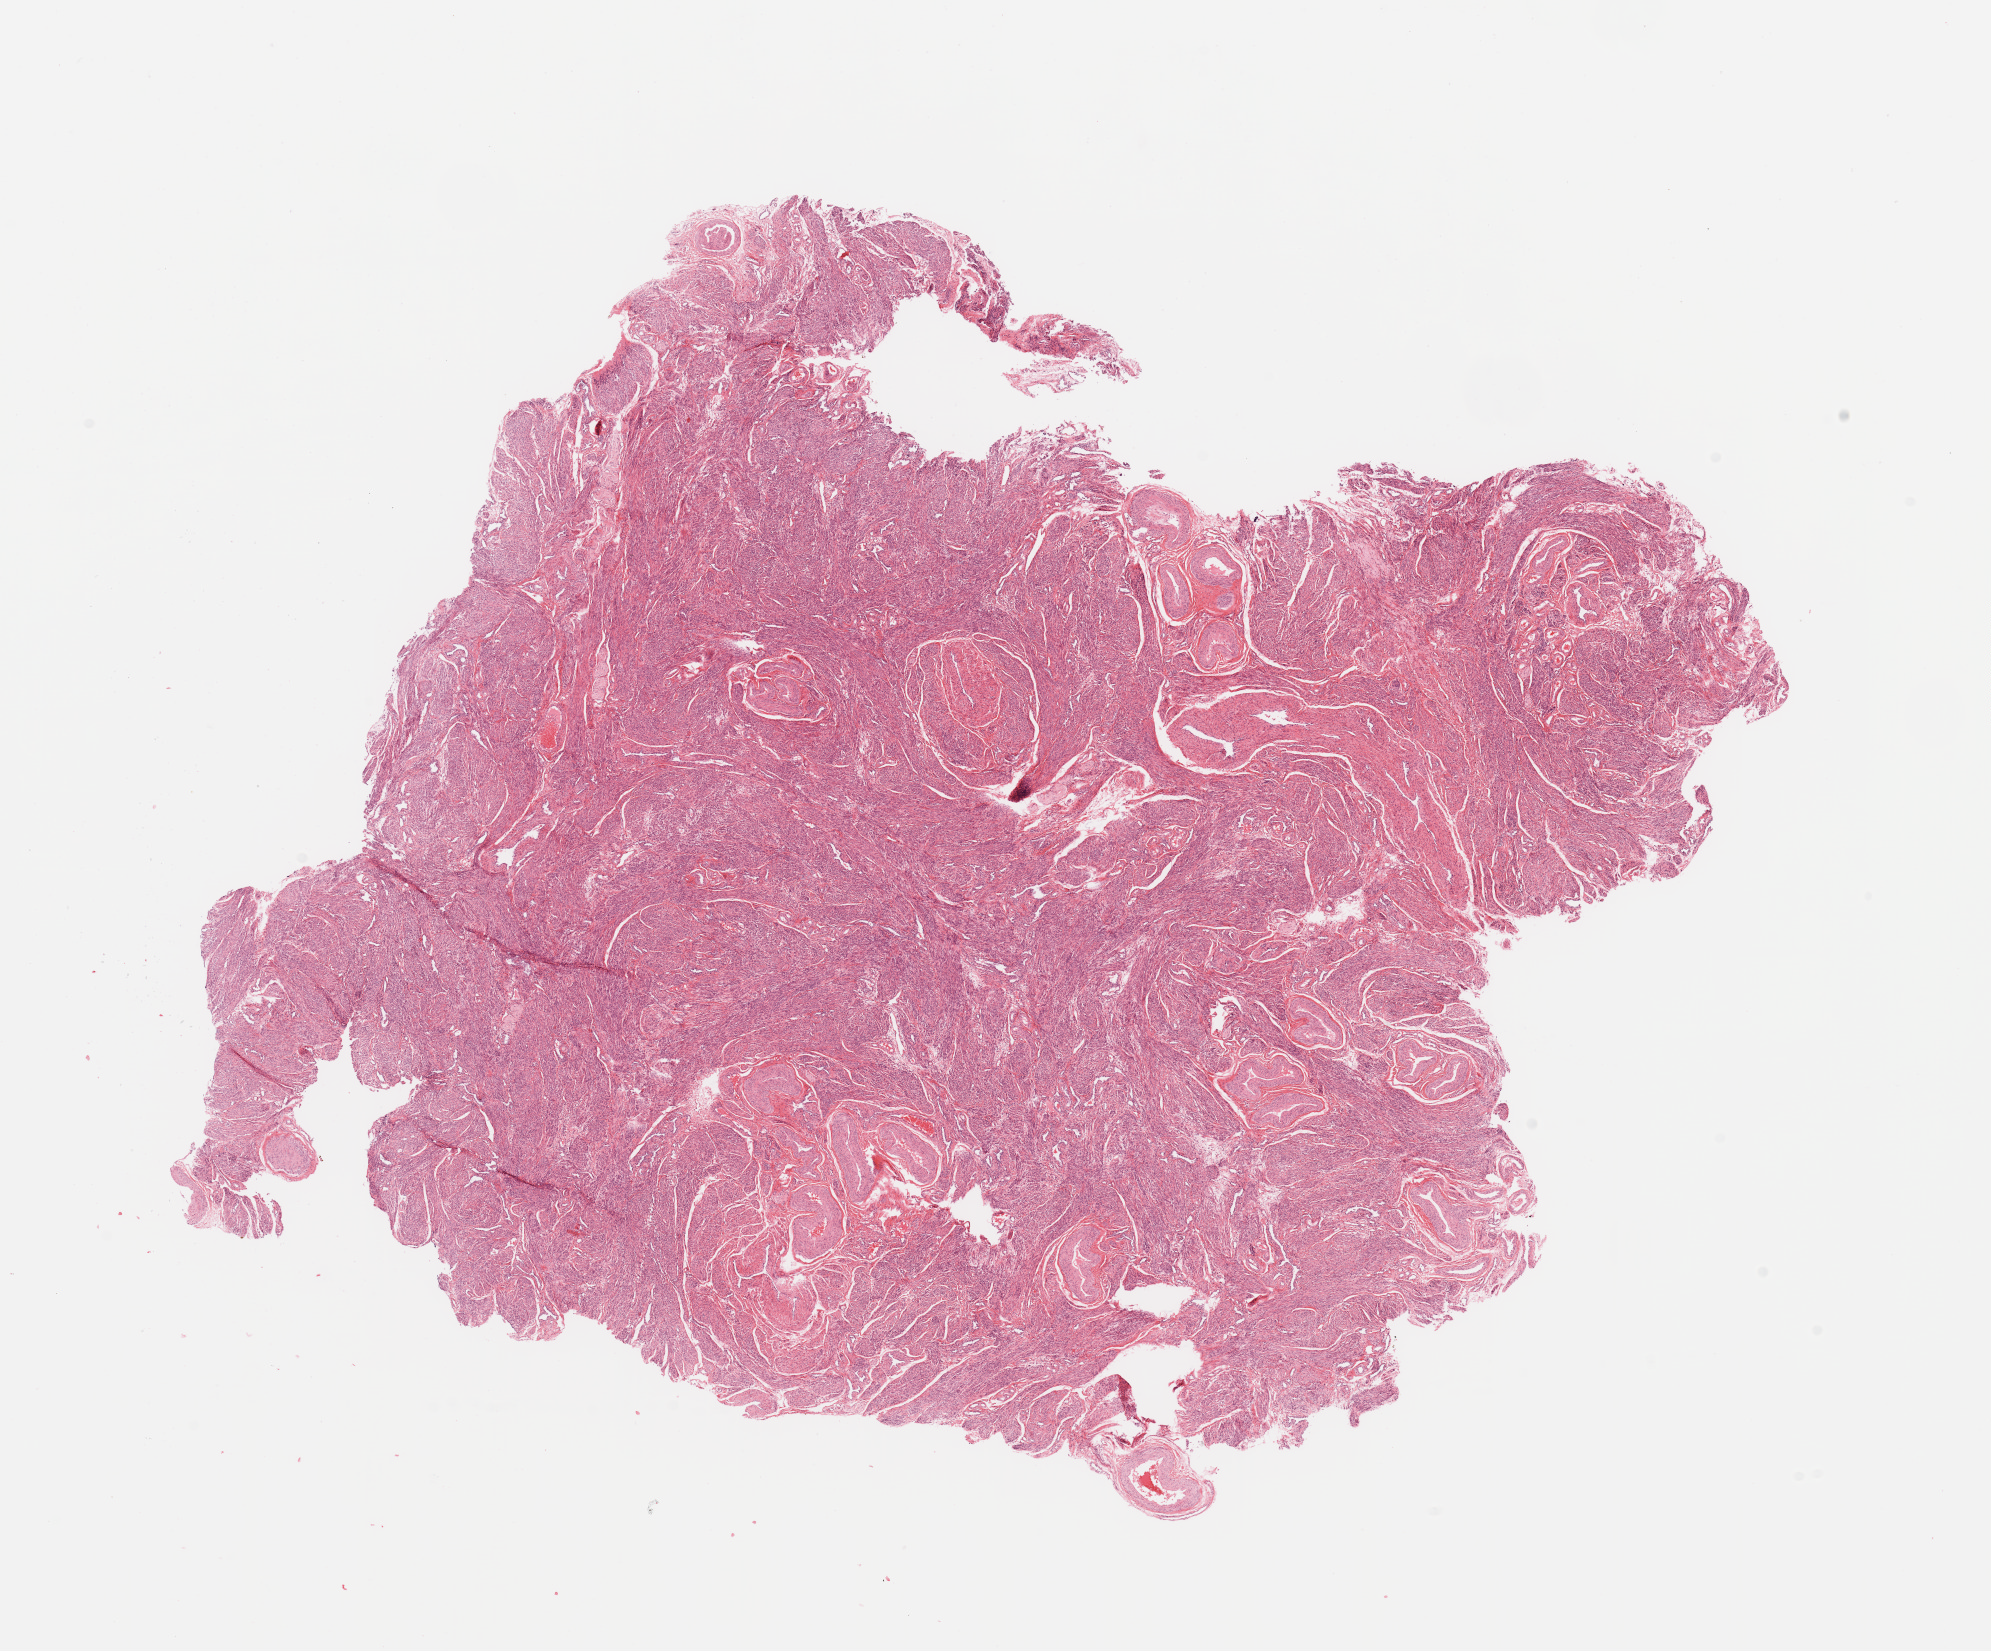
Digitized Hematoxylin and eosin (H&E) stained tissue section (whole slide), a low-resolution overview of the entire scanned area, about 15.8 x 13.1 mm. Normal (non-tumour) tissue sample, uterus. Female, 57 y/o.
• this section: normal (non-tumour) tissue from the same patient
• patient diagnosis: Endometrioid adenocarcinoma, NOS